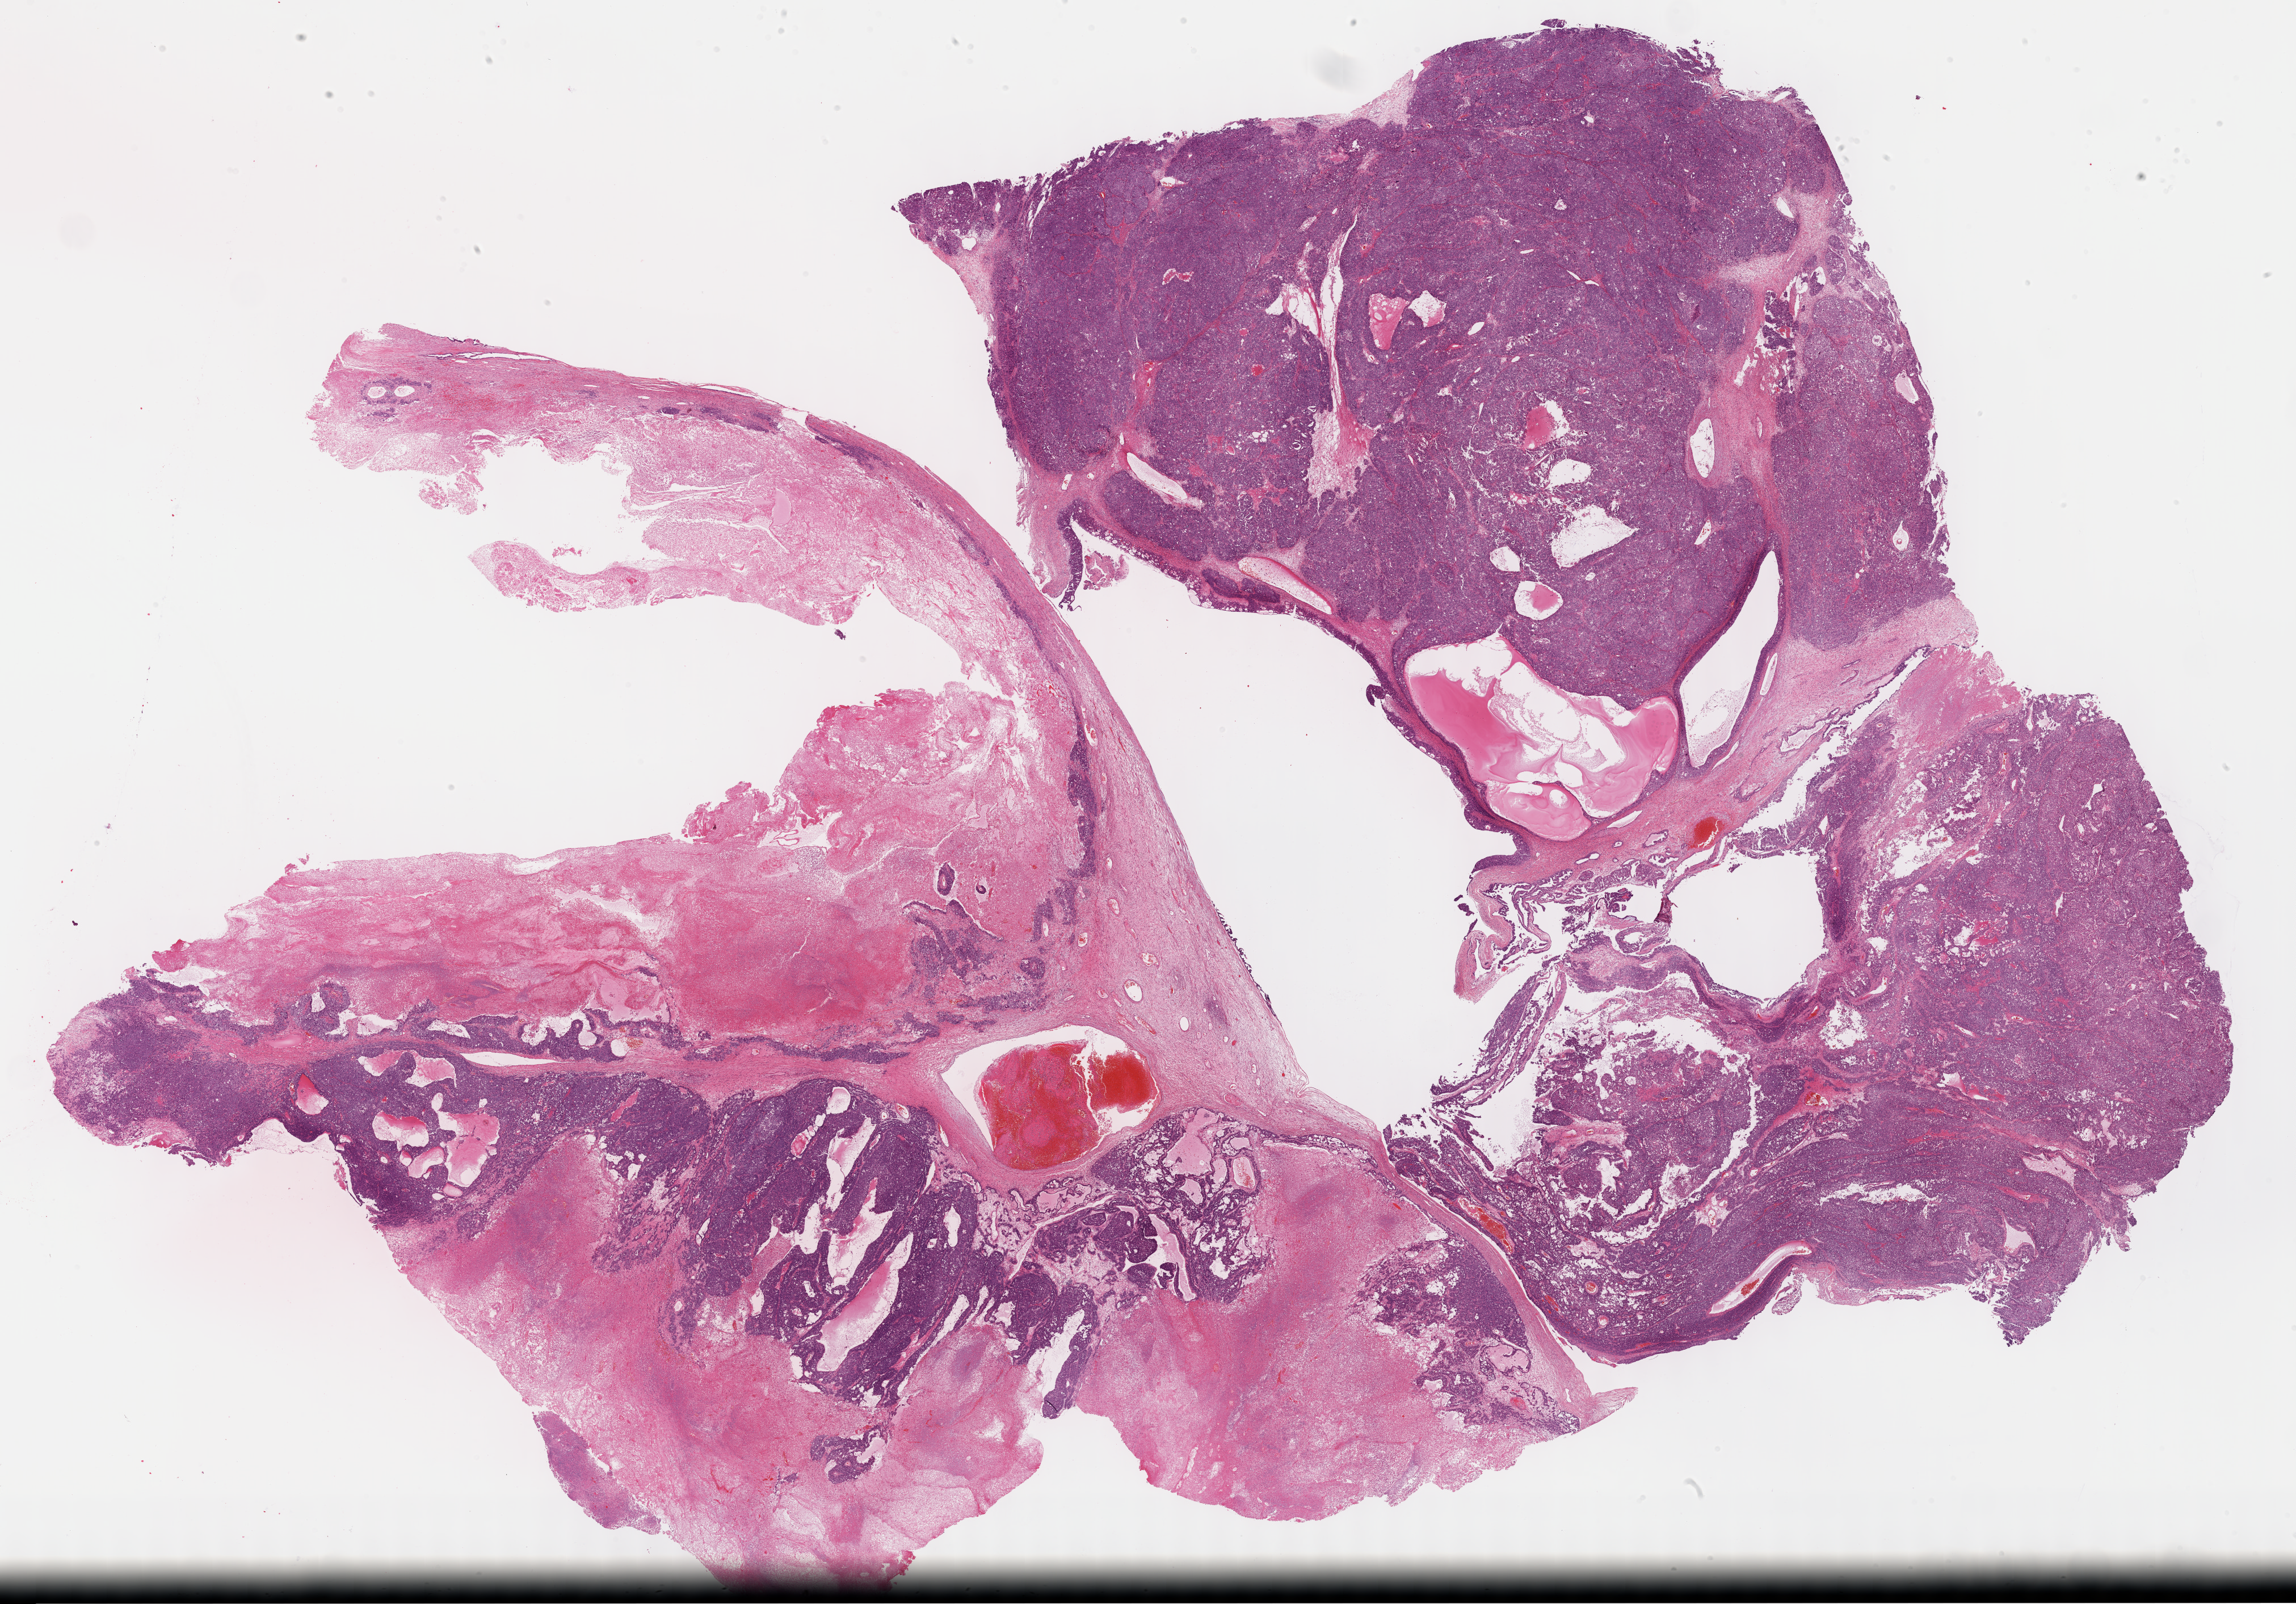
Whole-slide histology image, H&E-stained, shown as a low-resolution overview of the whole scanned area (about 32.7 x 22.9 mm); formalin-fixed paraffin-embedded (FFPE) diagnostic section; primary tumour sample from the ovary. Female, age 53 years at initial diagnosis. Histologic grade: G3 (poorly differentiated).
- pathologic diagnosis: Serous cystadenocarcinoma, NOS
- FIGO stage: IIIC